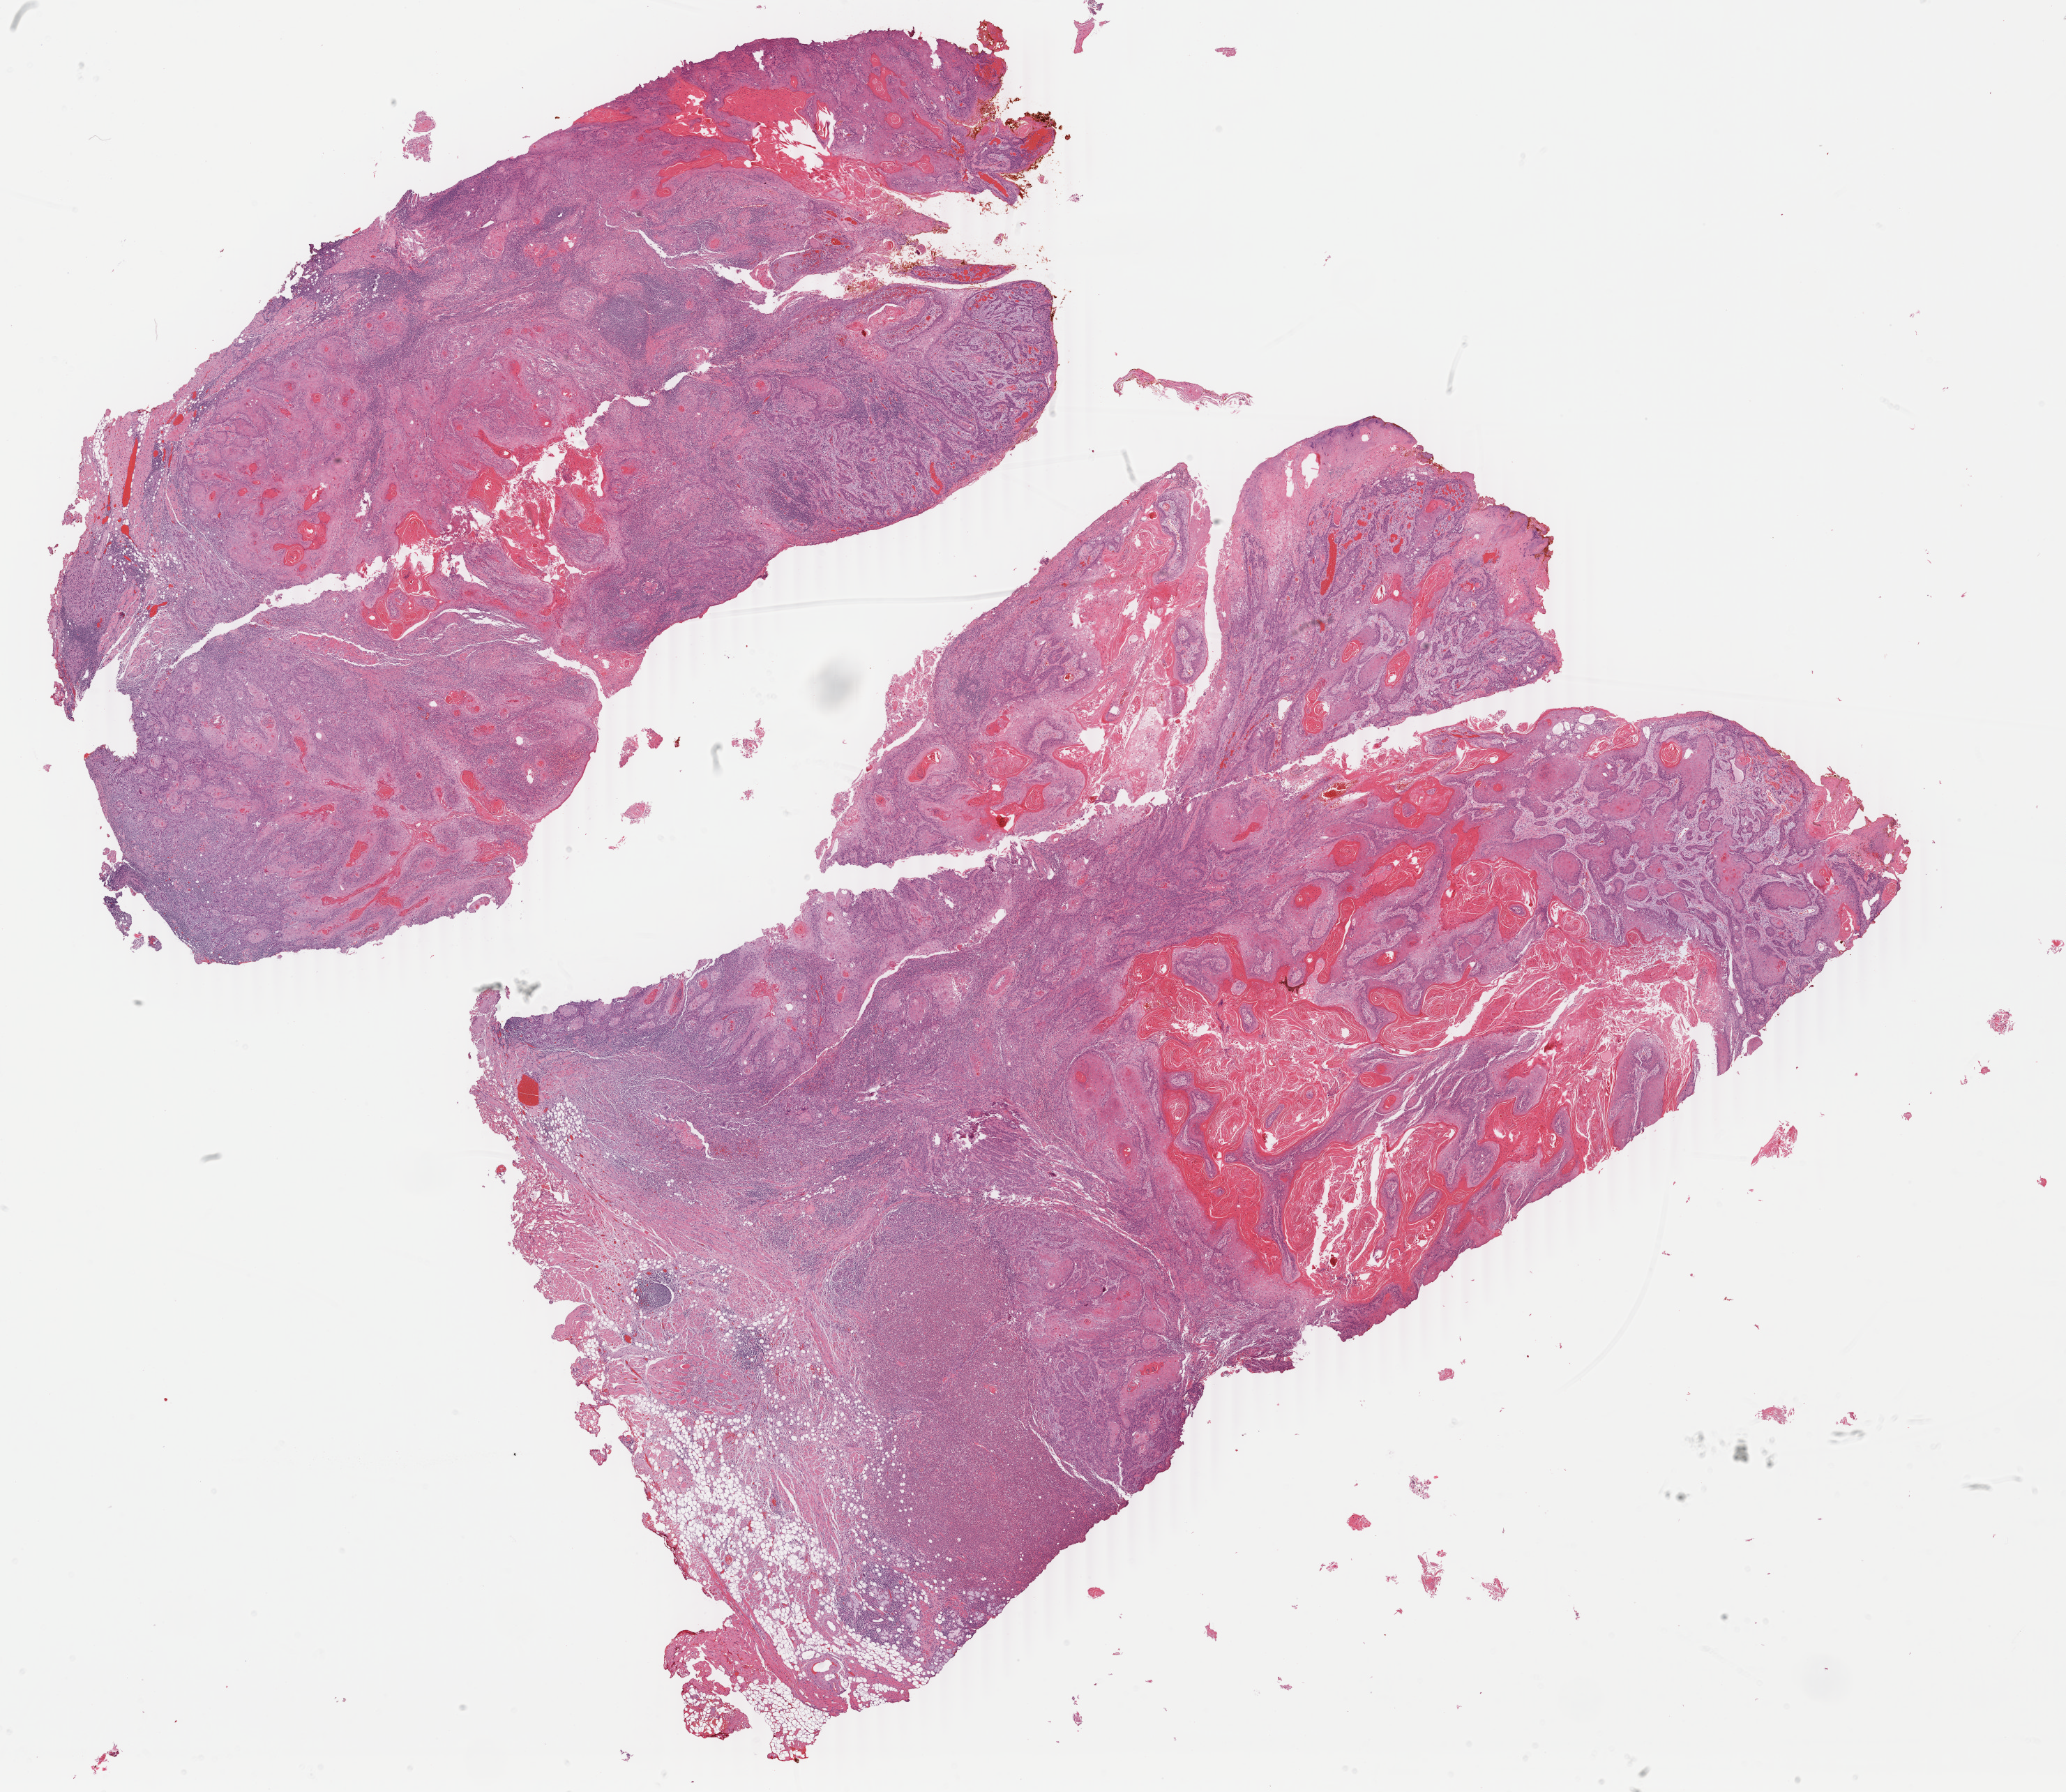
Whole-slide histology image, Hematoxylin and eosin (H&E) stained — whole scanned area (about 23.6 x 20.4 mm) shown as a low-resolution overview, formalin-fixed paraffin-embedded (FFPE) diagnostic section, head and neck, primary tumour sample. Patient: female, age at initial diagnosis 72 years. Histologic grade: G1 (well differentiated).
TNM: T2 N0 M0. Pathologic diagnosis: Squamous cell carcinoma, keratinizing, NOS (tongue, NOS). Lymph nodes positive (case pathology): 0 of 42 examined. AJCC pathologic stage: II (7th edition).